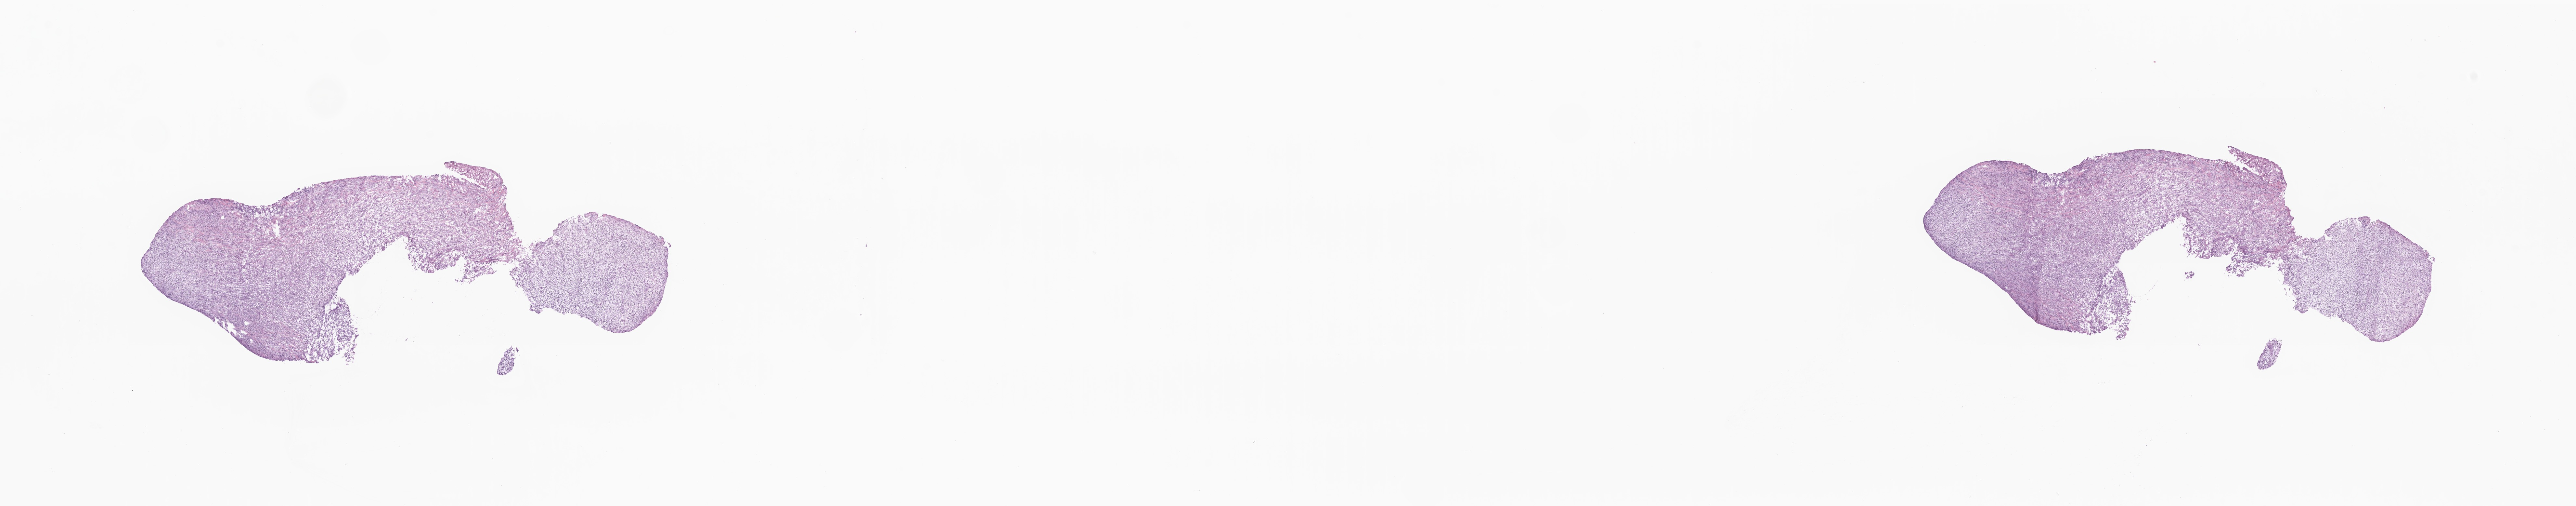
Digitized hematoxylin and eosin (H&E)-stained section — whole scanned area (about 33.4 x 6.6 mm) shown as a low-resolution overview. Frozen section (tissue freezing medium). Specimen: recurrent tumor. Anatomic site: brain. Male, age 49 years at initial diagnosis. Slide review estimates, as recorded: tumor cells 90%, tumor nuclei 90%, stromal cells 10%, necrosis 0%, normal cells 0%. Inflammatory infiltration, as recorded: lymphocyte infiltration 0%, monocyte infiltration 0%, neutrophil infiltration 0%.
Patient diagnosis: Glioblastoma, NOS.